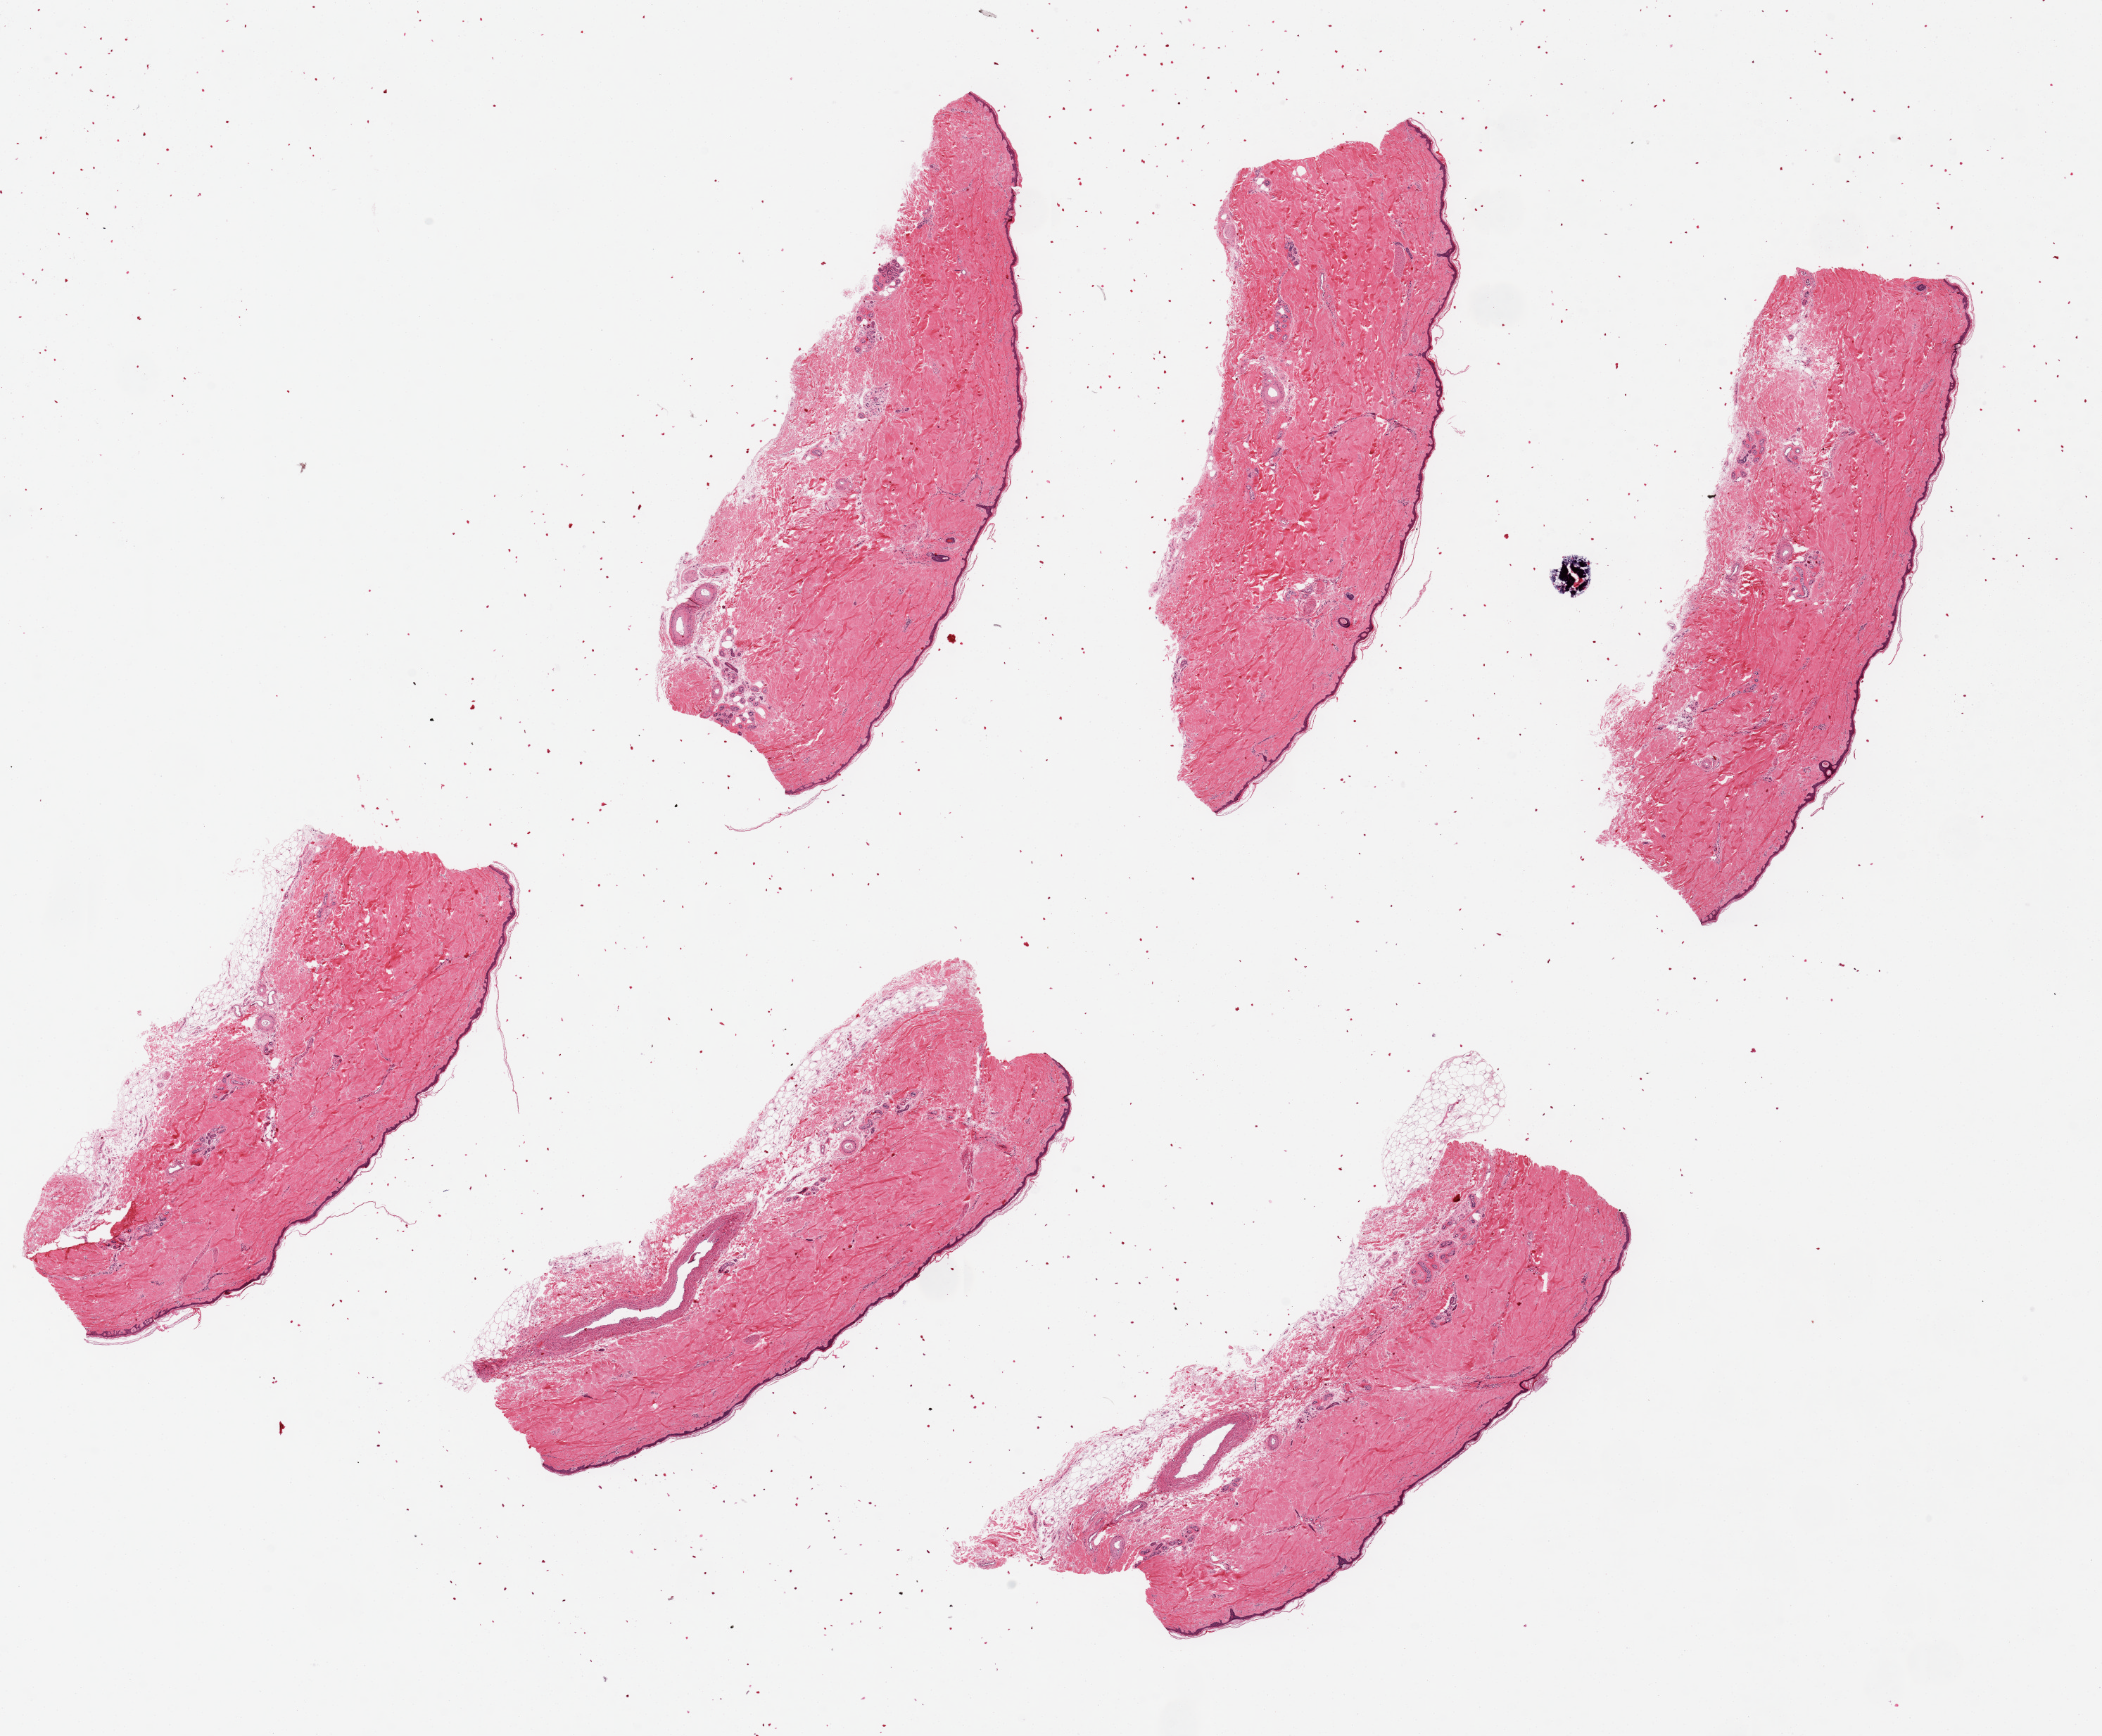
Whole-slide image, haematoxylin and eosin stain, brightfield, whole scanned area (about 23.6 x 19.5 mm) shown as a low-resolution overview, PAXgene-fixed, paraffin-embedded tissue, section of skin of lower leg (target tissue), tissue donor sample. Donor: female.
Pathologist's review note for this sample: 6 pieces up to 7x3 mm; 0.5 mm subcutaneous adipose on three pieces.